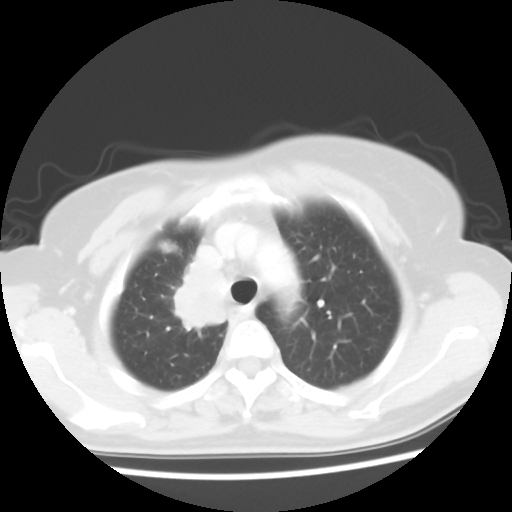
Chest CT, one axial slice. Slice 45 of 56 in the series (ordered by position). 120 kVp. Lung window (W 1500 / L -600 HU). 512 × 512 image matrix. Patient: female, 62 years. Case-level facts recorded for this patient, not image findings: clinical TNM (as recorded): T2 N1 M1a.
Annotated regions visible in this slice (rectangle marked by the reading radiologist):
- lung tumour (recorded histology: adenocarcinoma): bounding box <169,254,230,334> (left, top, right, bottom; pixels)